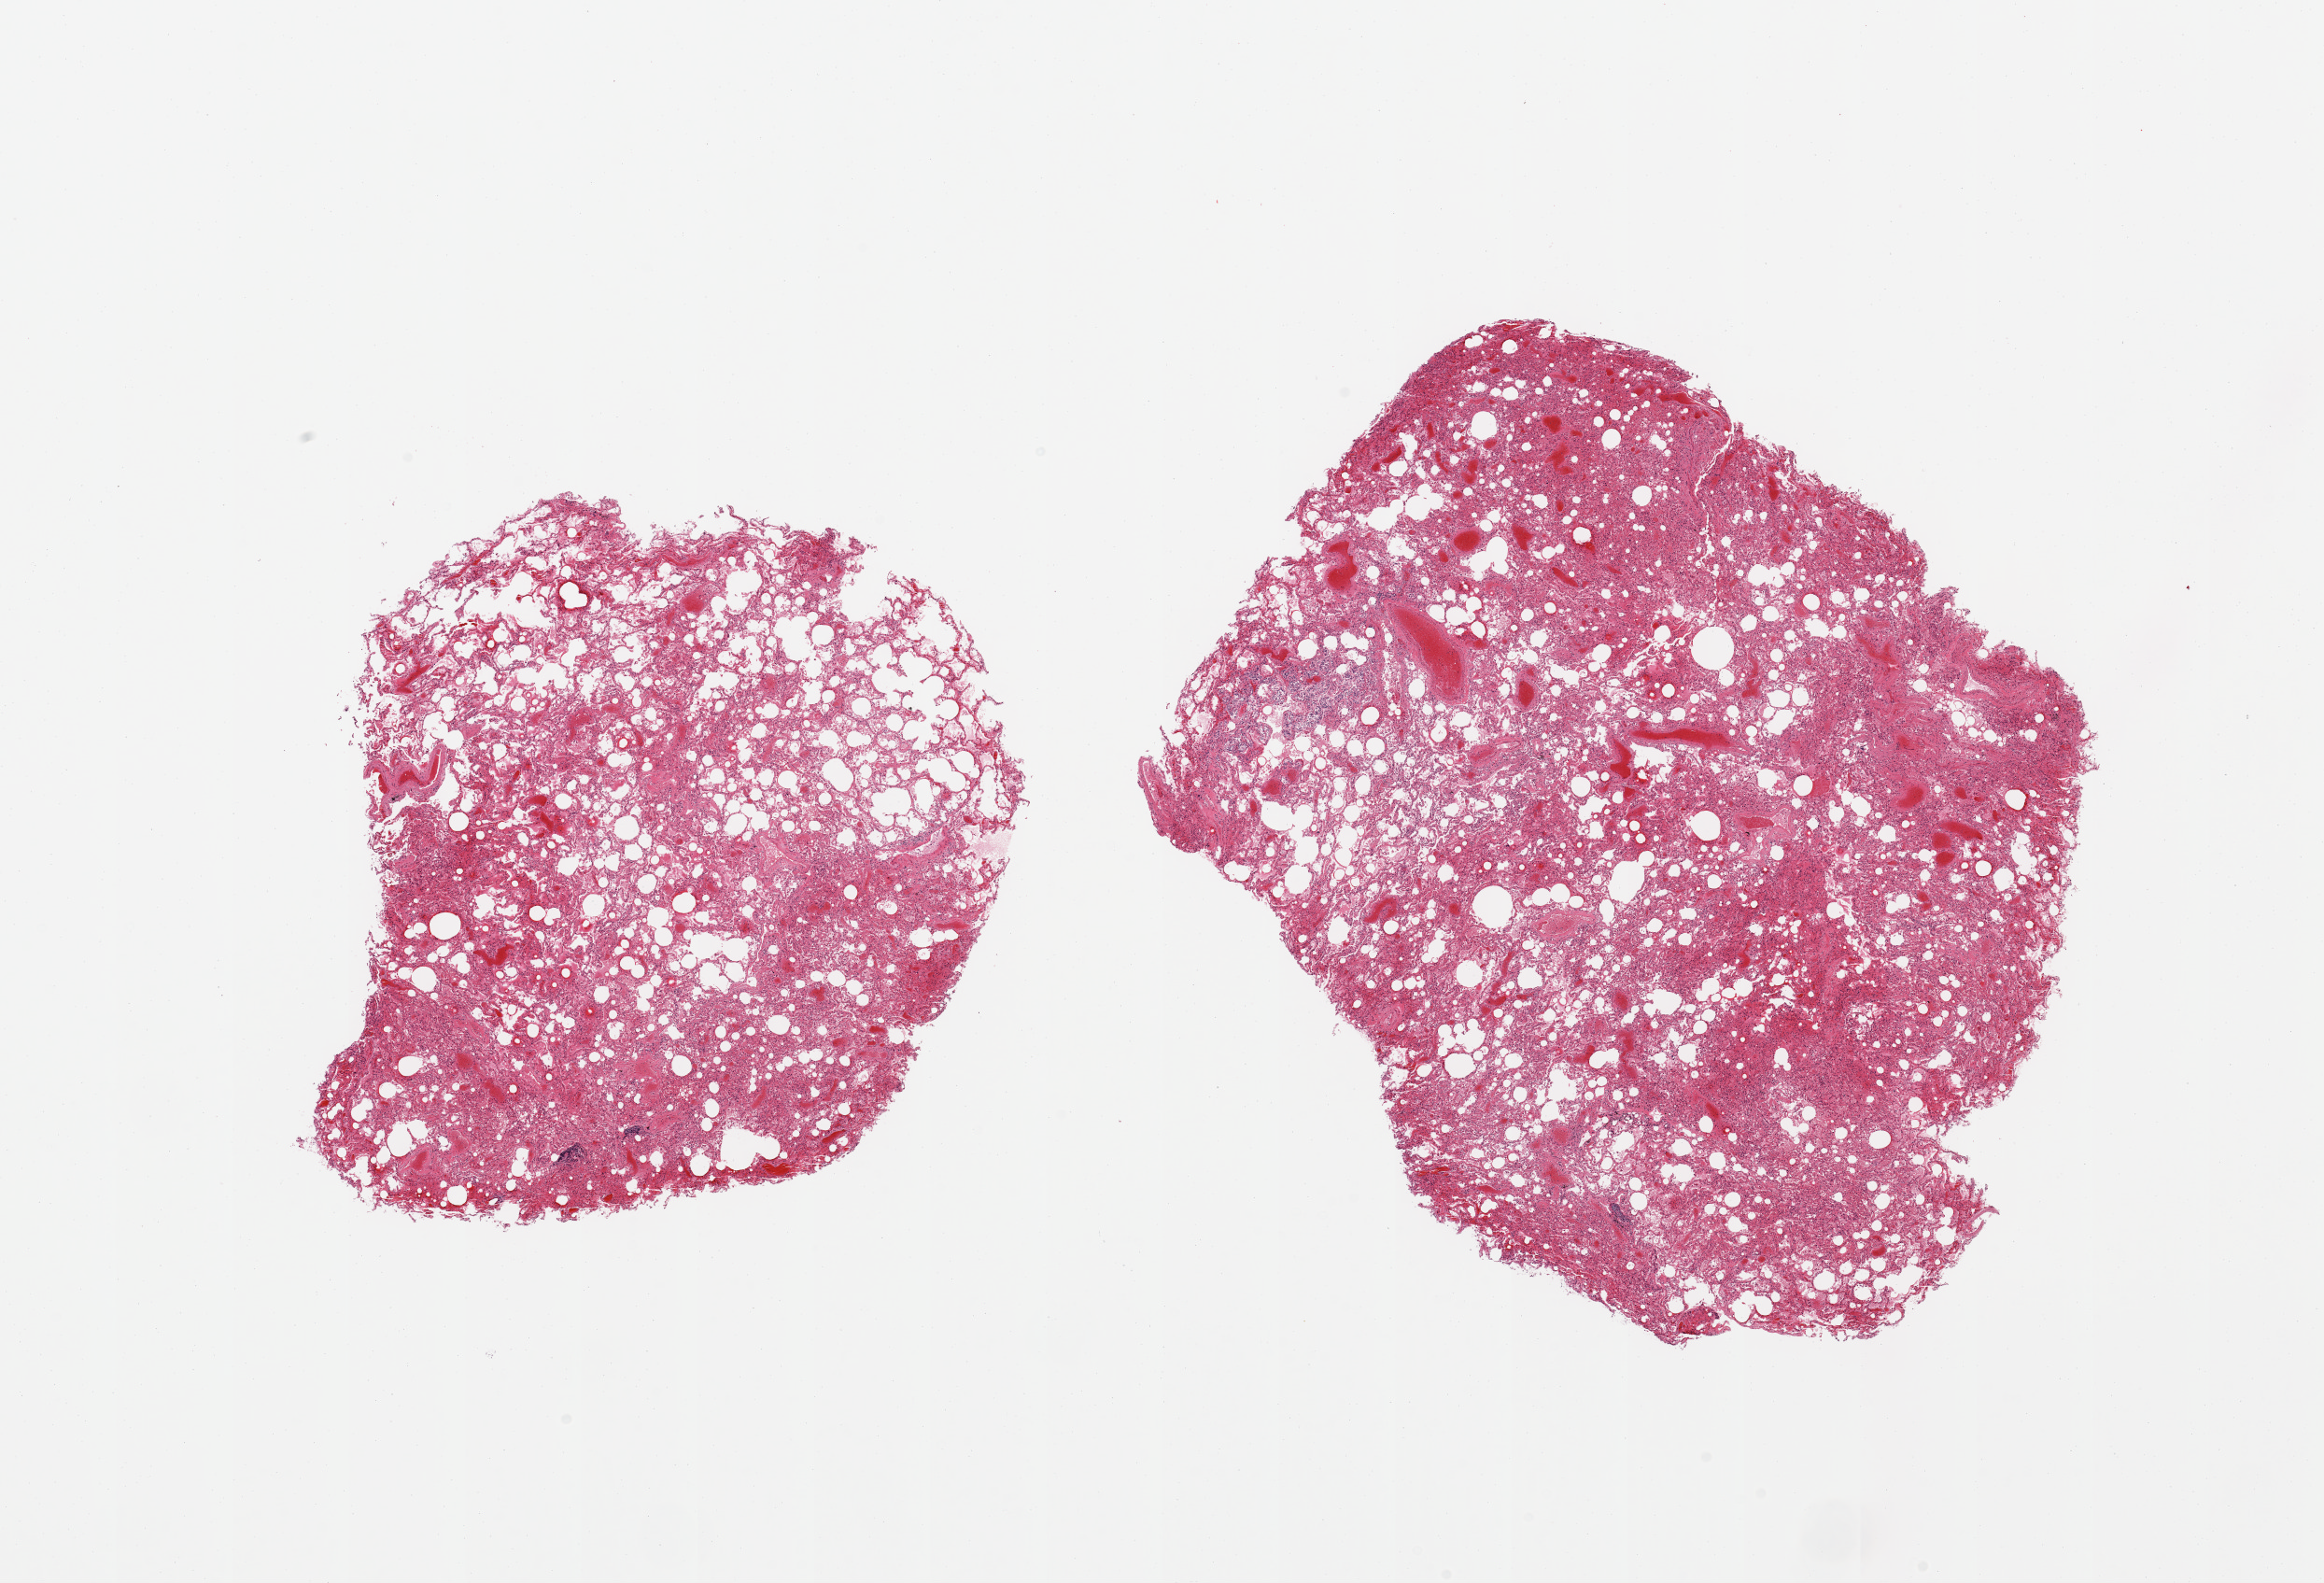
Digitized hematoxylin and eosin (H&E)-stained section, shown as a low-resolution overview of the whole scanned area (about 19.7 x 13.4 mm), PAXgene-fixed, paraffin-embedded tissue, section of lung (target tissue), donor tissue sample.
• review note (as recorded): 2 pieces; patchy atelectasis& congestion